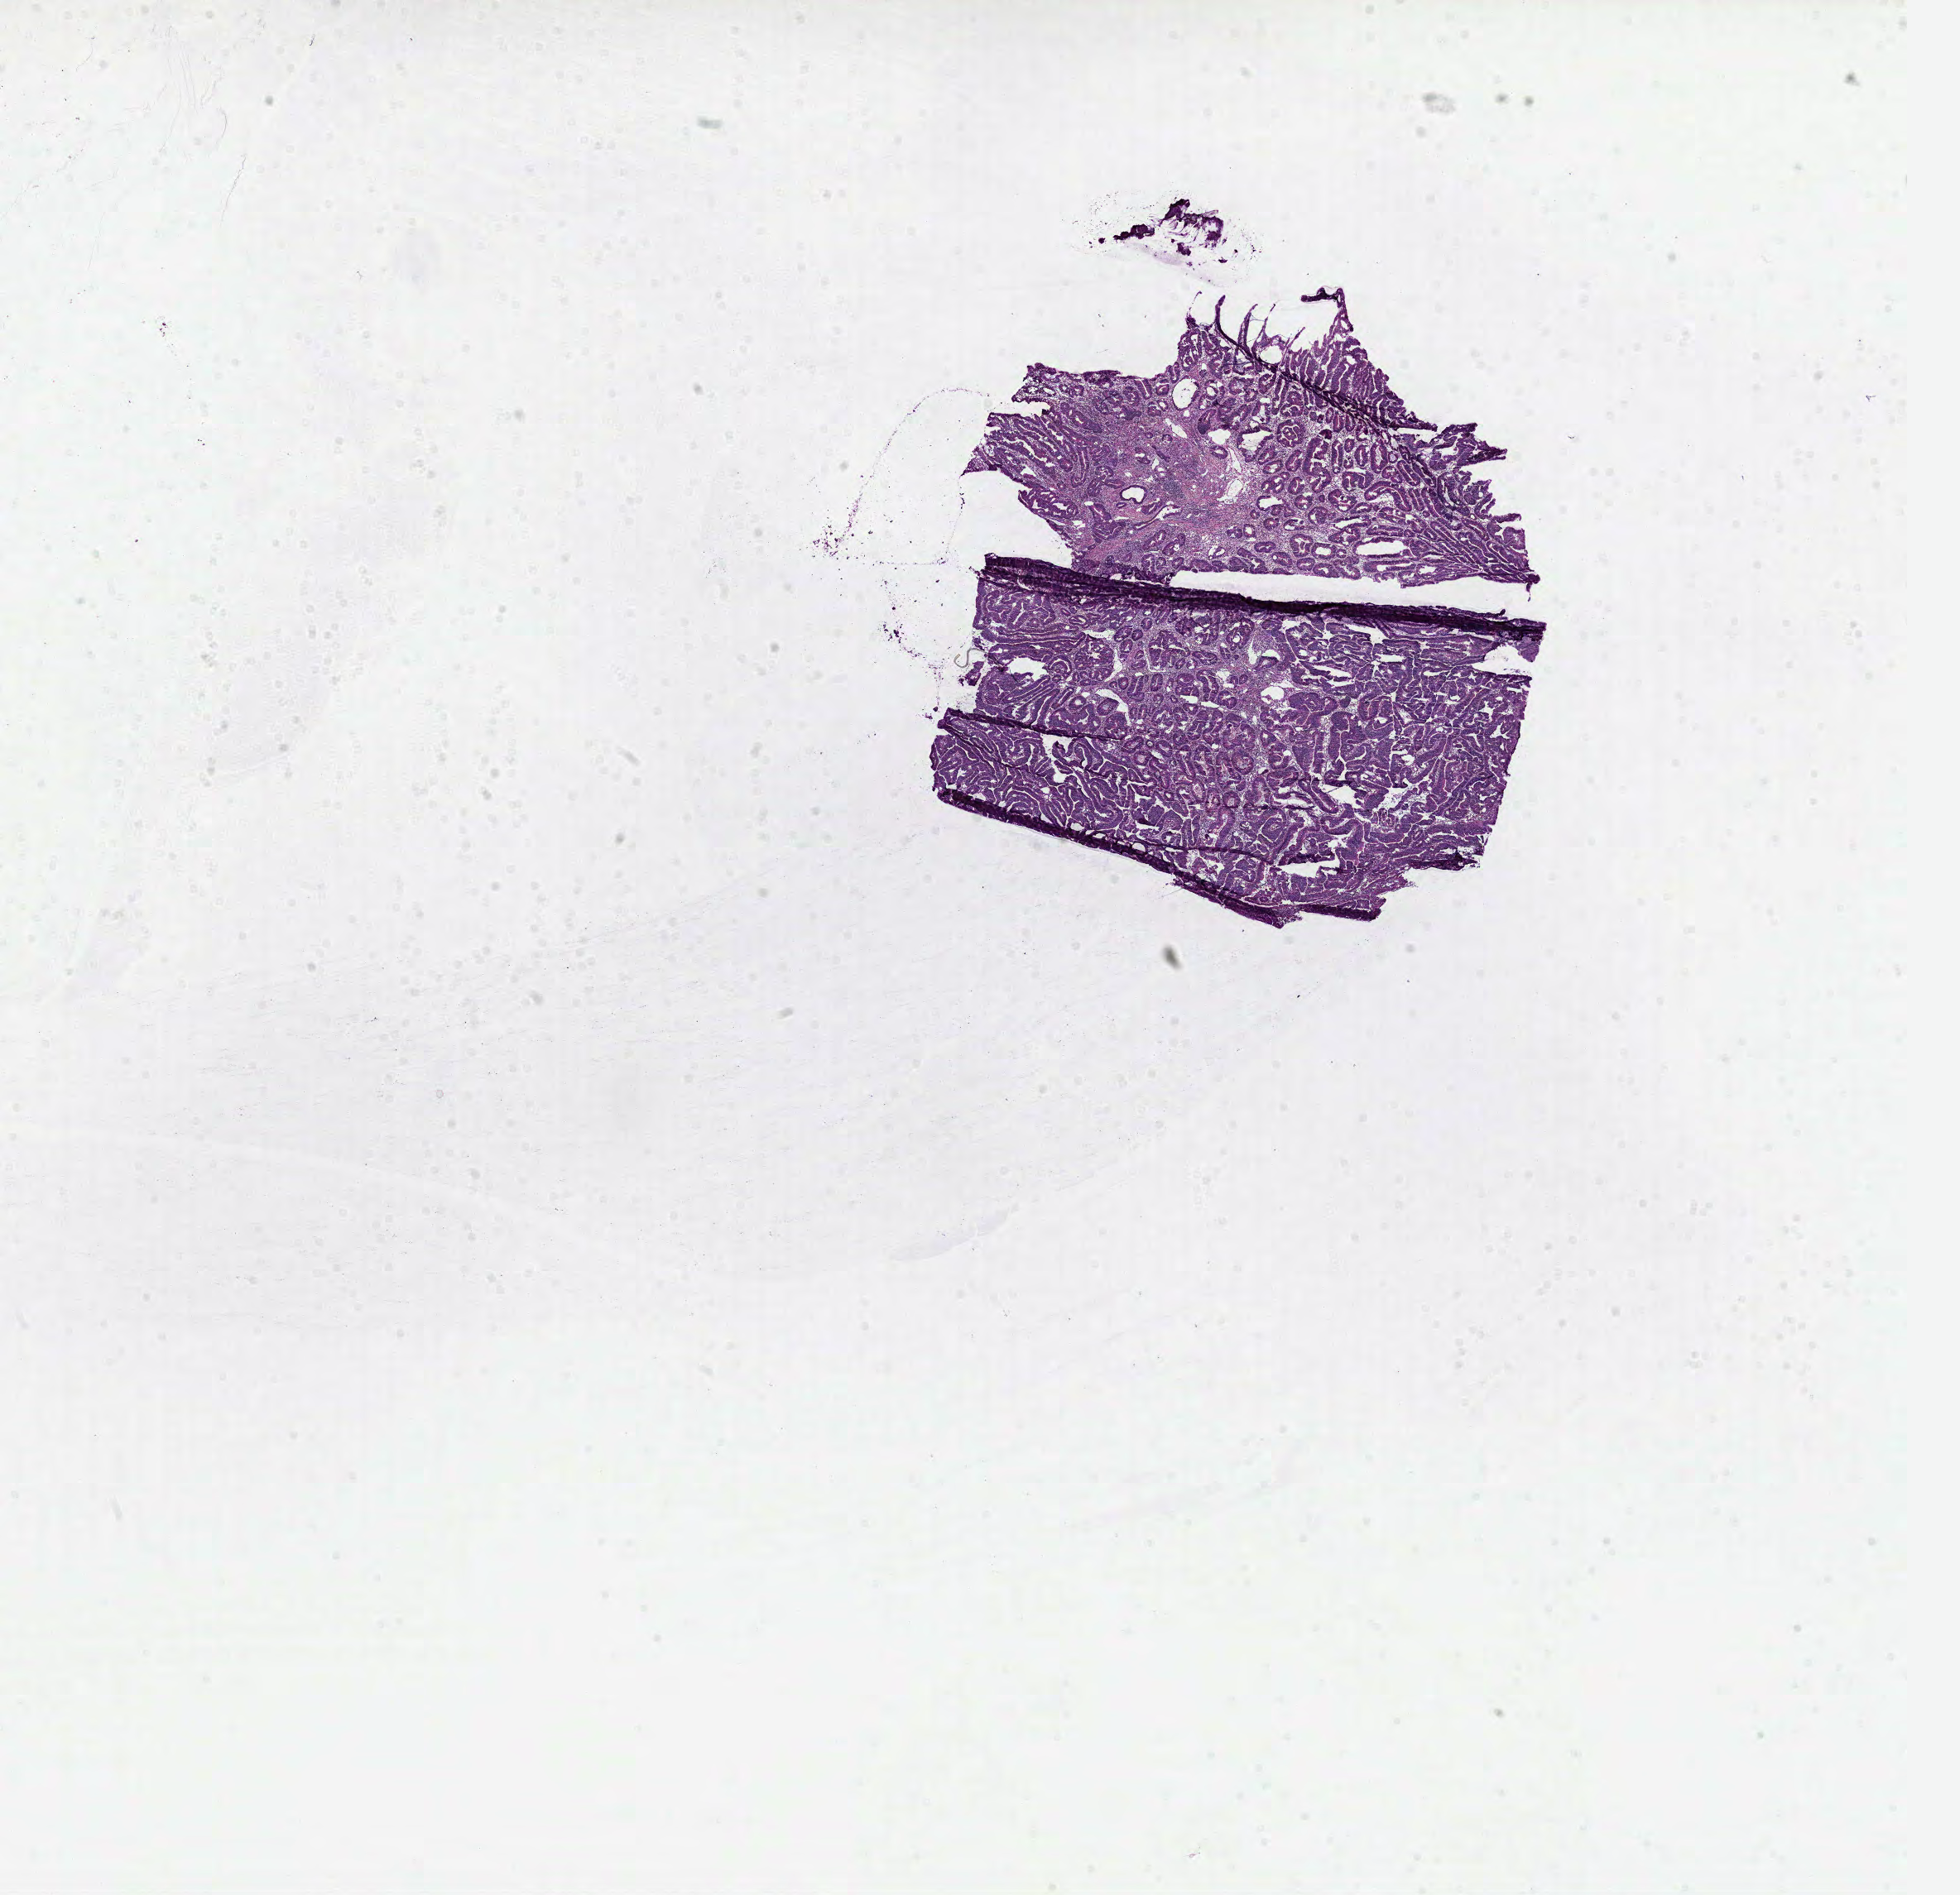
Hematoxylin and eosin (H&E) stained whole-slide image, shown as a low-resolution overview of the whole scanned area (about 19.1 x 18.5 mm); formalin-fixed paraffin-embedded (FFPE) diagnostic section; sample: primary tumour, colon. Patient: female, age at initial diagnosis 63 years.
Histologic diagnosis: Adenocarcinoma, NOS.